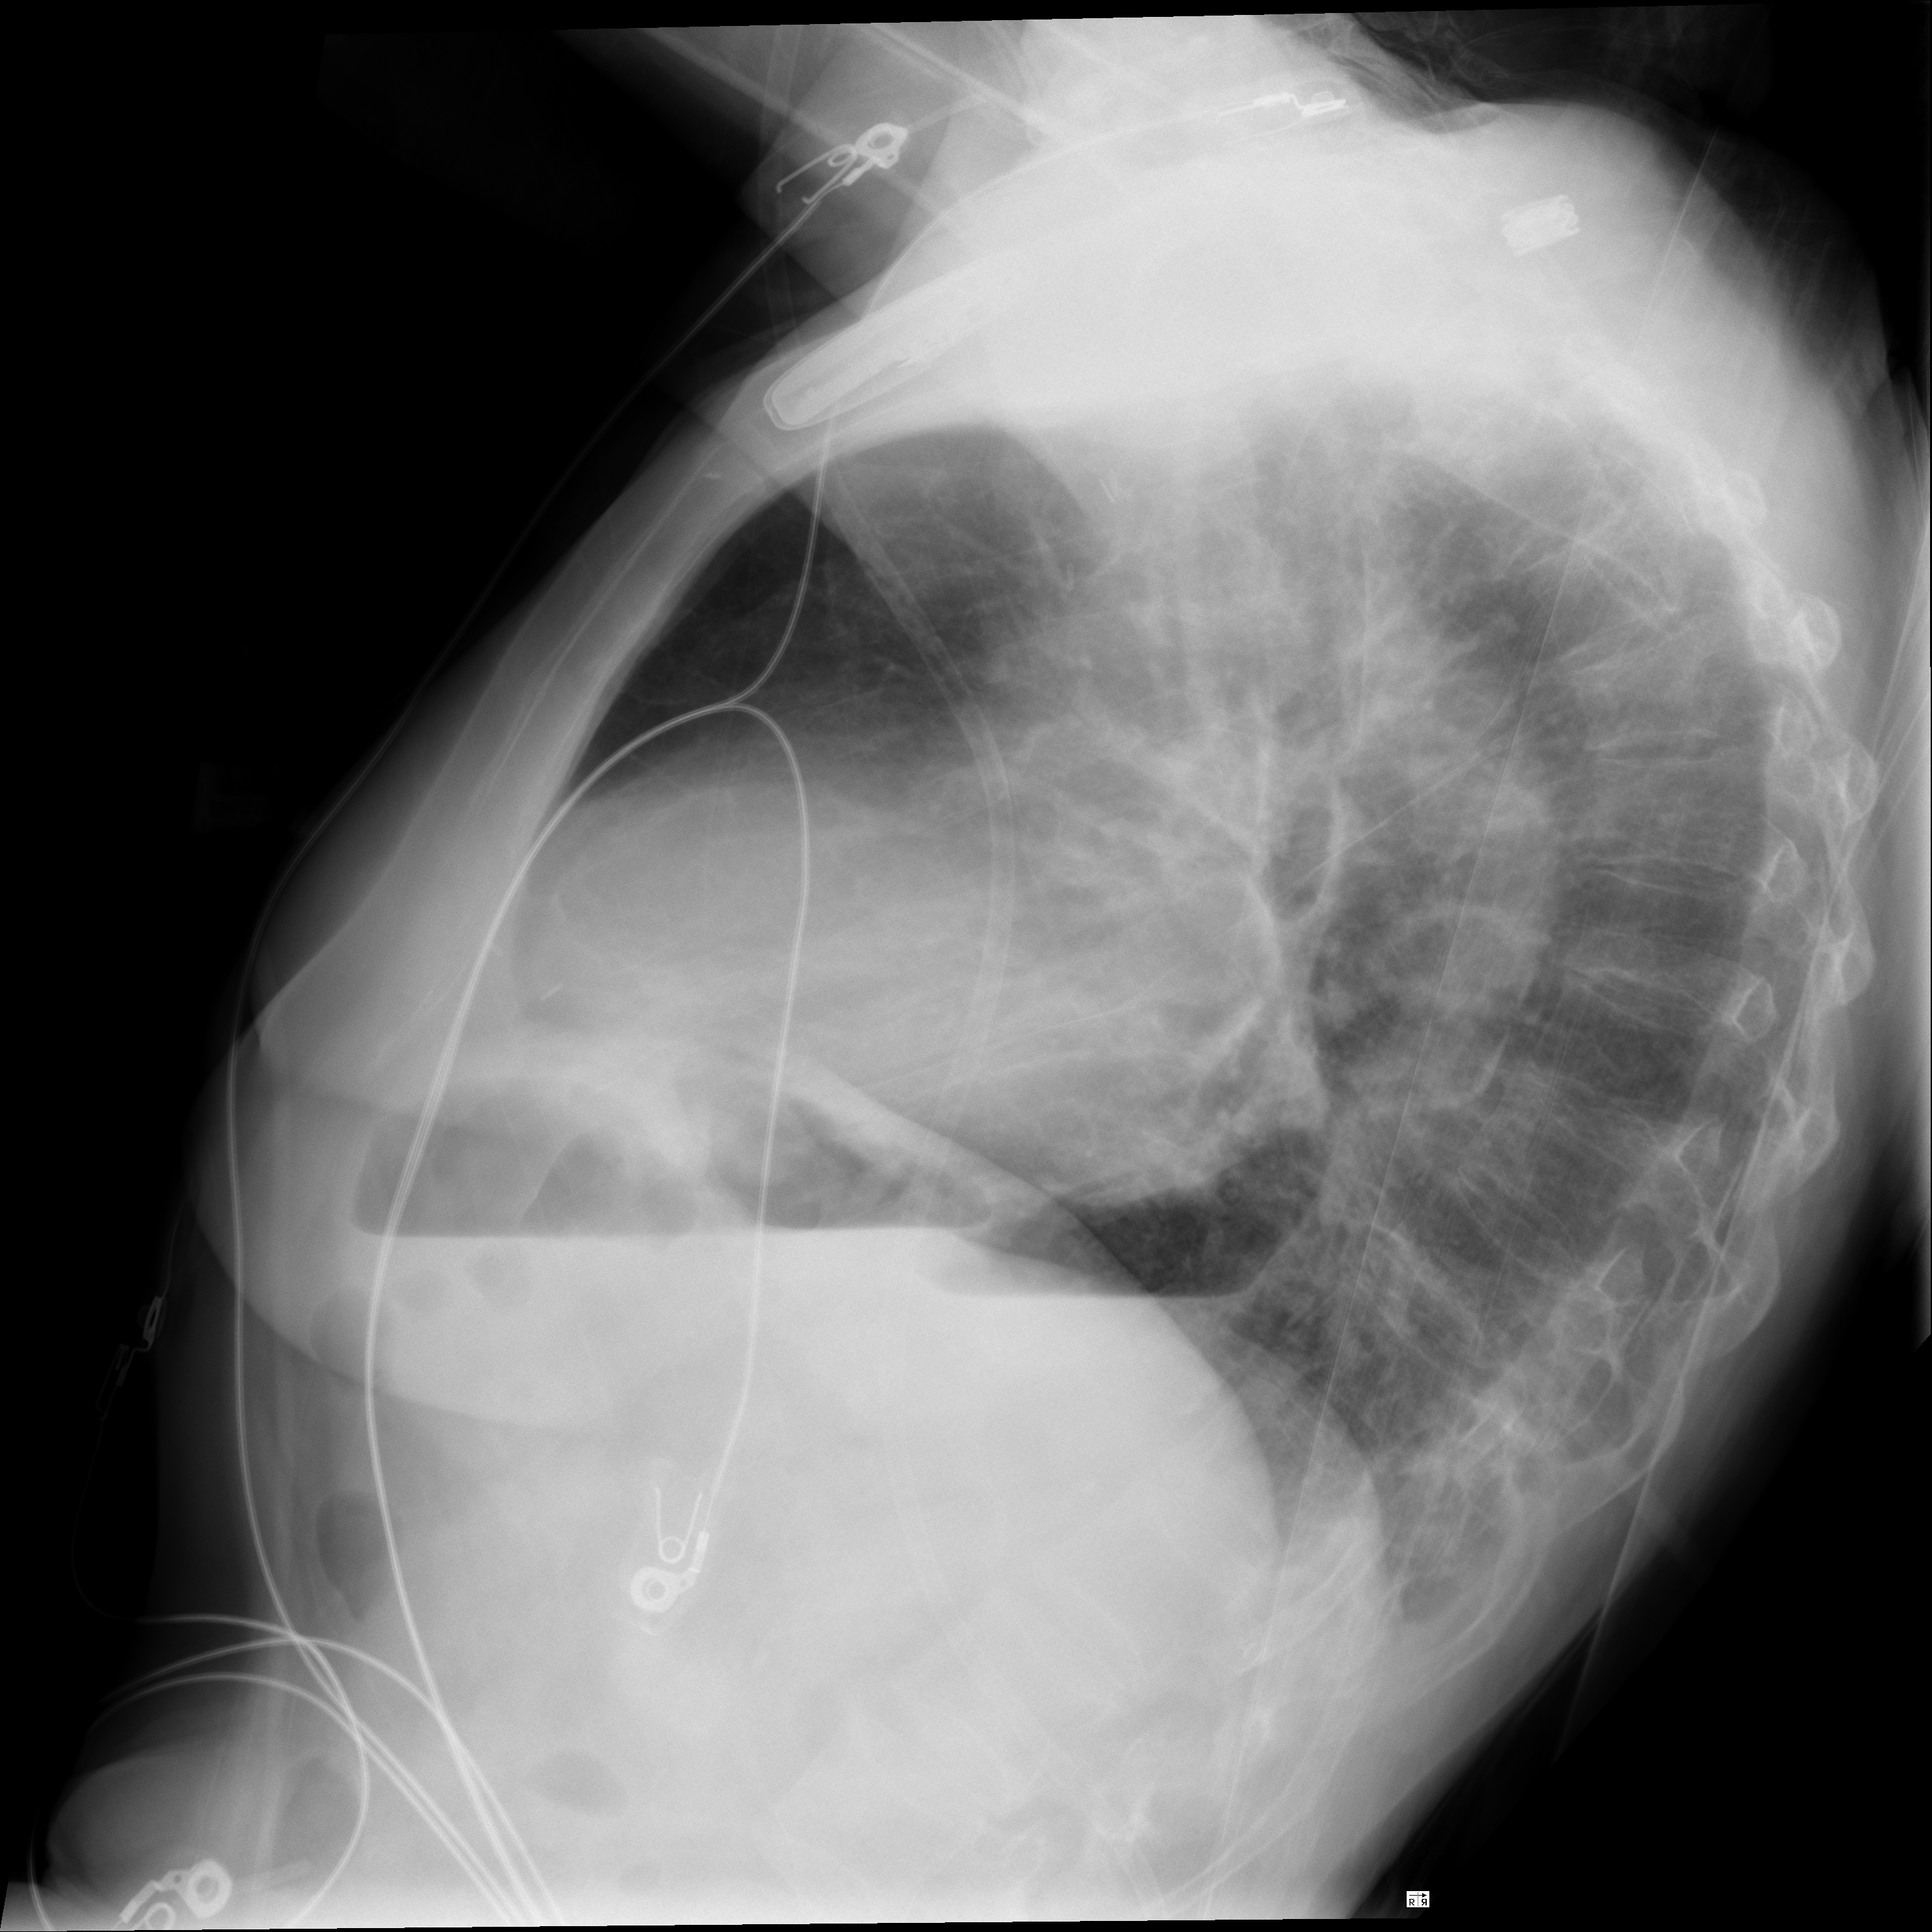
Chest radiograph, lateral projection. Female patient, age 70 years; imaged 0 days after the COVID-19 diagnosis.
Key findings recorded by the radiologist: Lungs are clear, no nodule, airspace disease or pleural effusion.